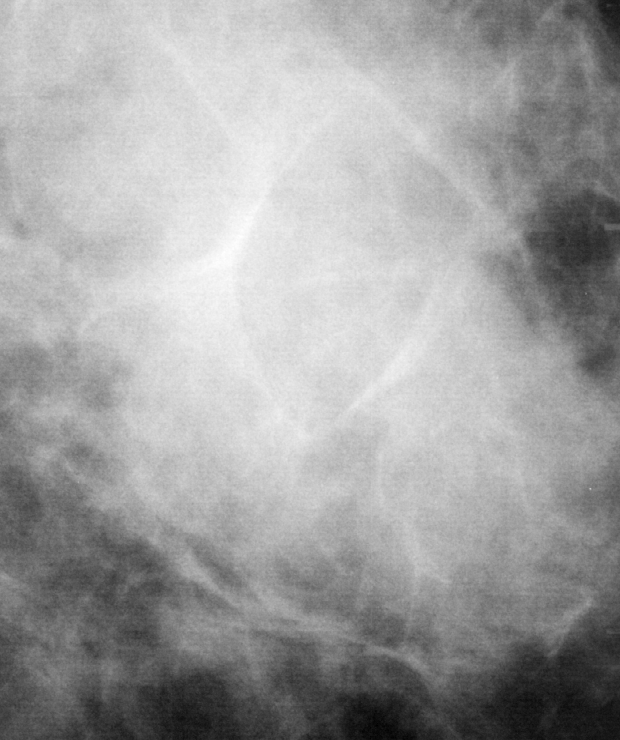
Crop from a digitized film mammogram around one marked abnormality, right breast, CC view.
- Marked abnormality: mass, shape asymmetric breast tissue, margins ill defined; BI-RADS assessment category 5; pathology (as recorded): malignant.